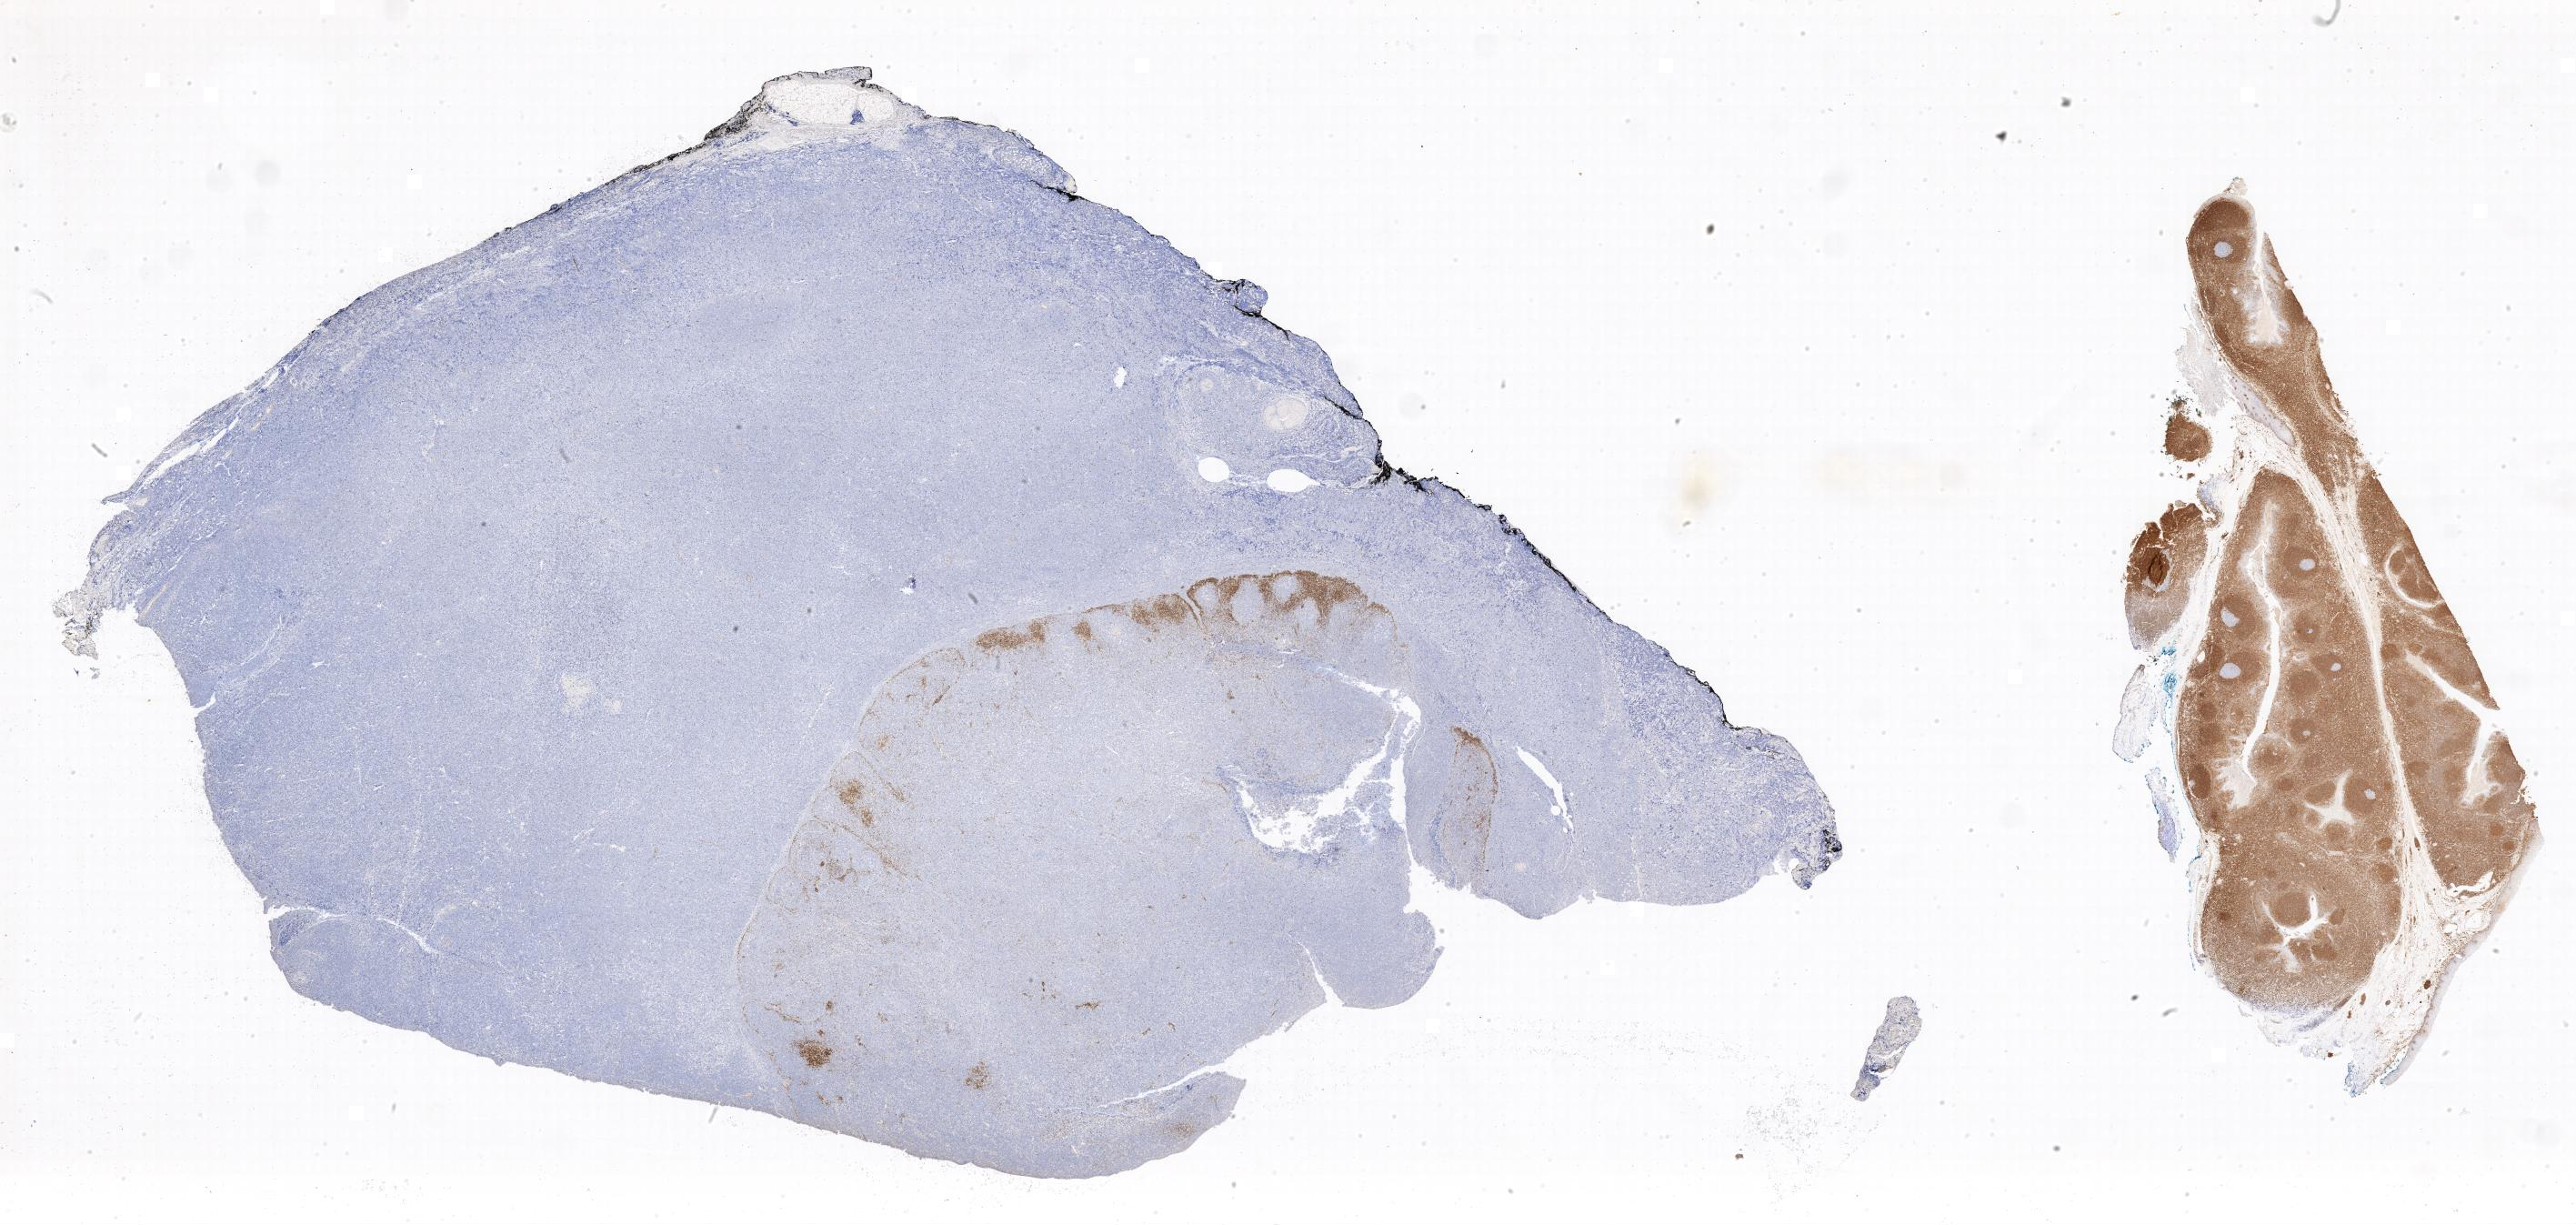
Immunohistochemistry (IHC) whole-slide image stained for BCL2, low-resolution overview of the scanned area. Tumor tissue. Site: lymph node of head and neck. Male, age 6 years at initial diagnosis.
Diagnosis: Burkitt lymphoma, NOS.